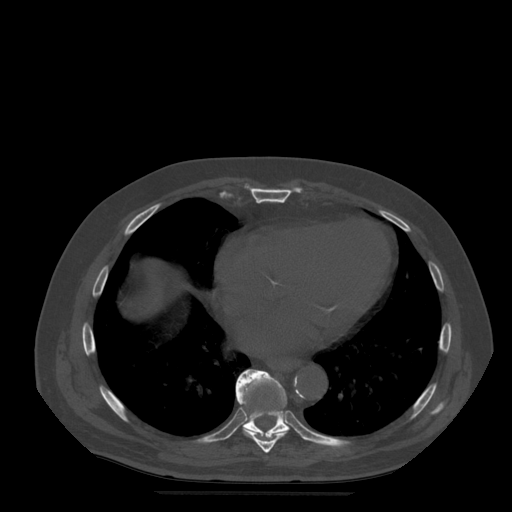
CT including the spine, one axial slice. Position 302 of 522 along the scan axis. Bone window (W 1800 / L 400 HU). 1.25 mm slice thickness. 512 × 512 image matrix. Patient age 72 years. Case-level facts recorded for this patient, not image findings: primary cancer: prostate.
Structures marked on this image (semi-automatically segmented with operator editing):
- T8 vertebra: bounding box <236,372,290,454> (left, top, right, bottom; pixels)
- T9 vertebra: <236,369,289,438>